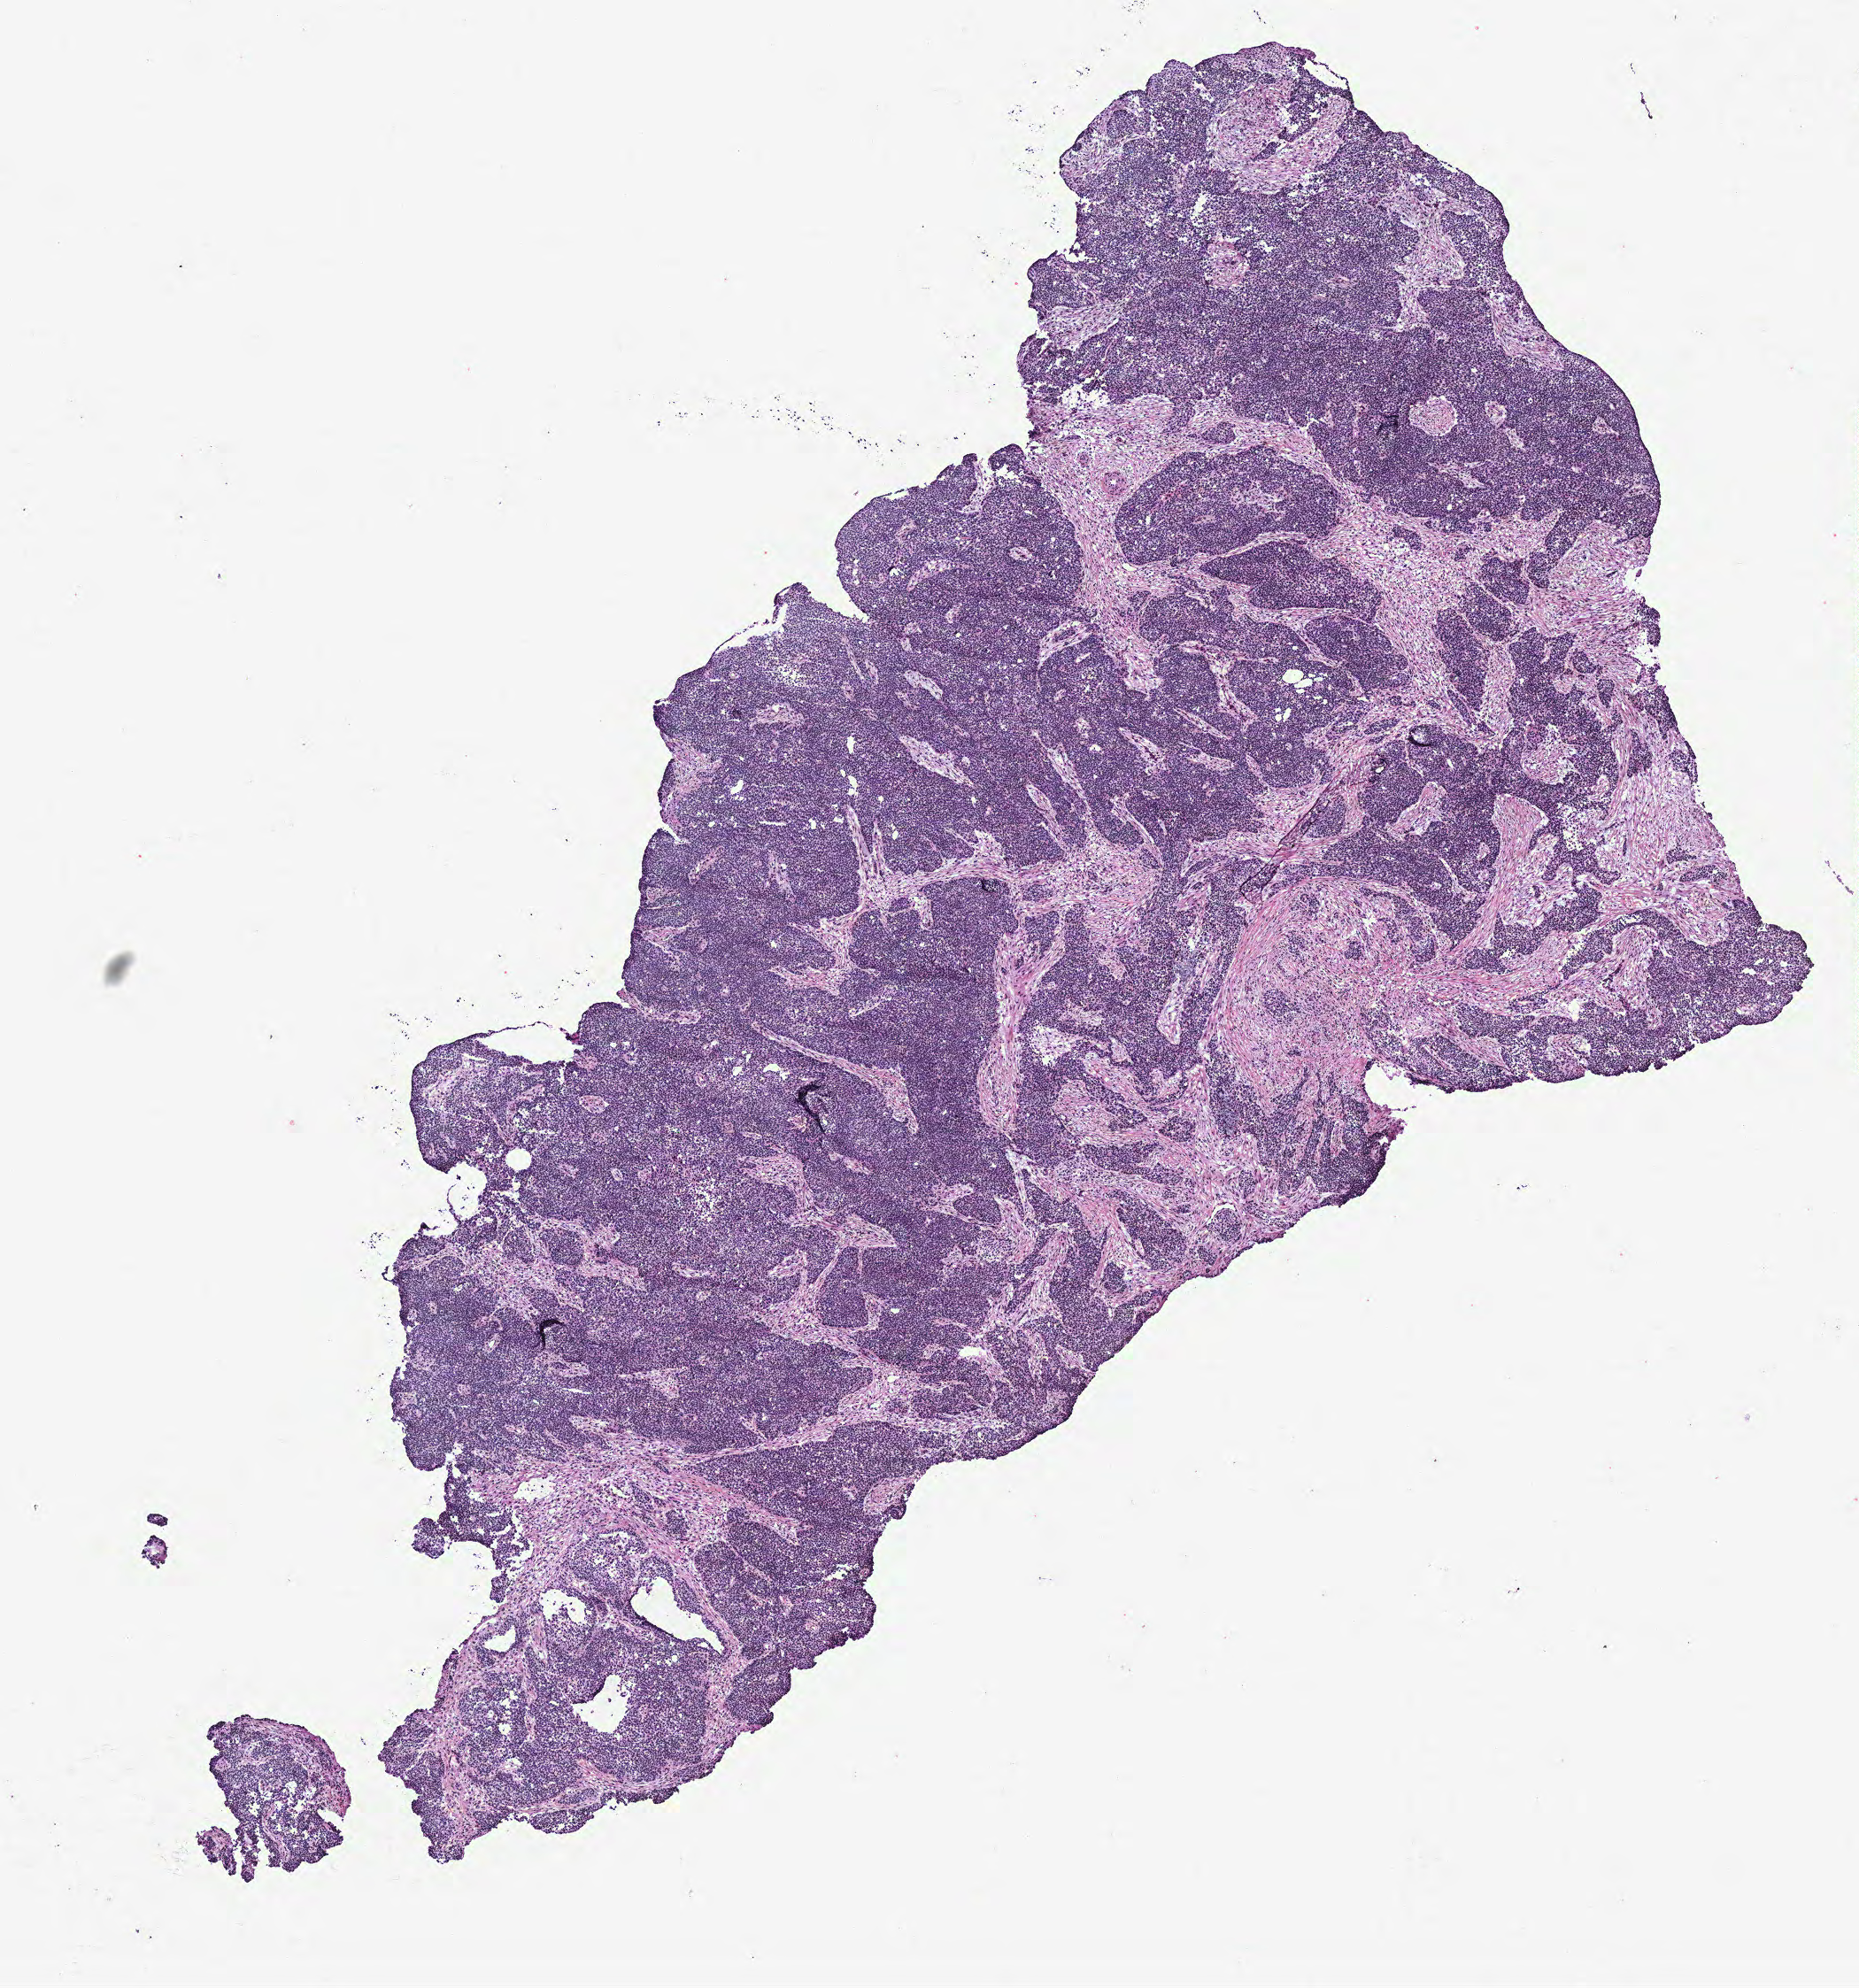
Digitized H&E-stained tissue section (whole slide), whole scanned area (about 8.4 x 9.0 mm, acquisition: 40x scan) shown as a low-resolution overview, tumour tissue sample, ovary. 48-year-old female patient.
Diagnosis: Serous adenocarcinoma, NOS. Primary tumour site (as recorded): ovary.